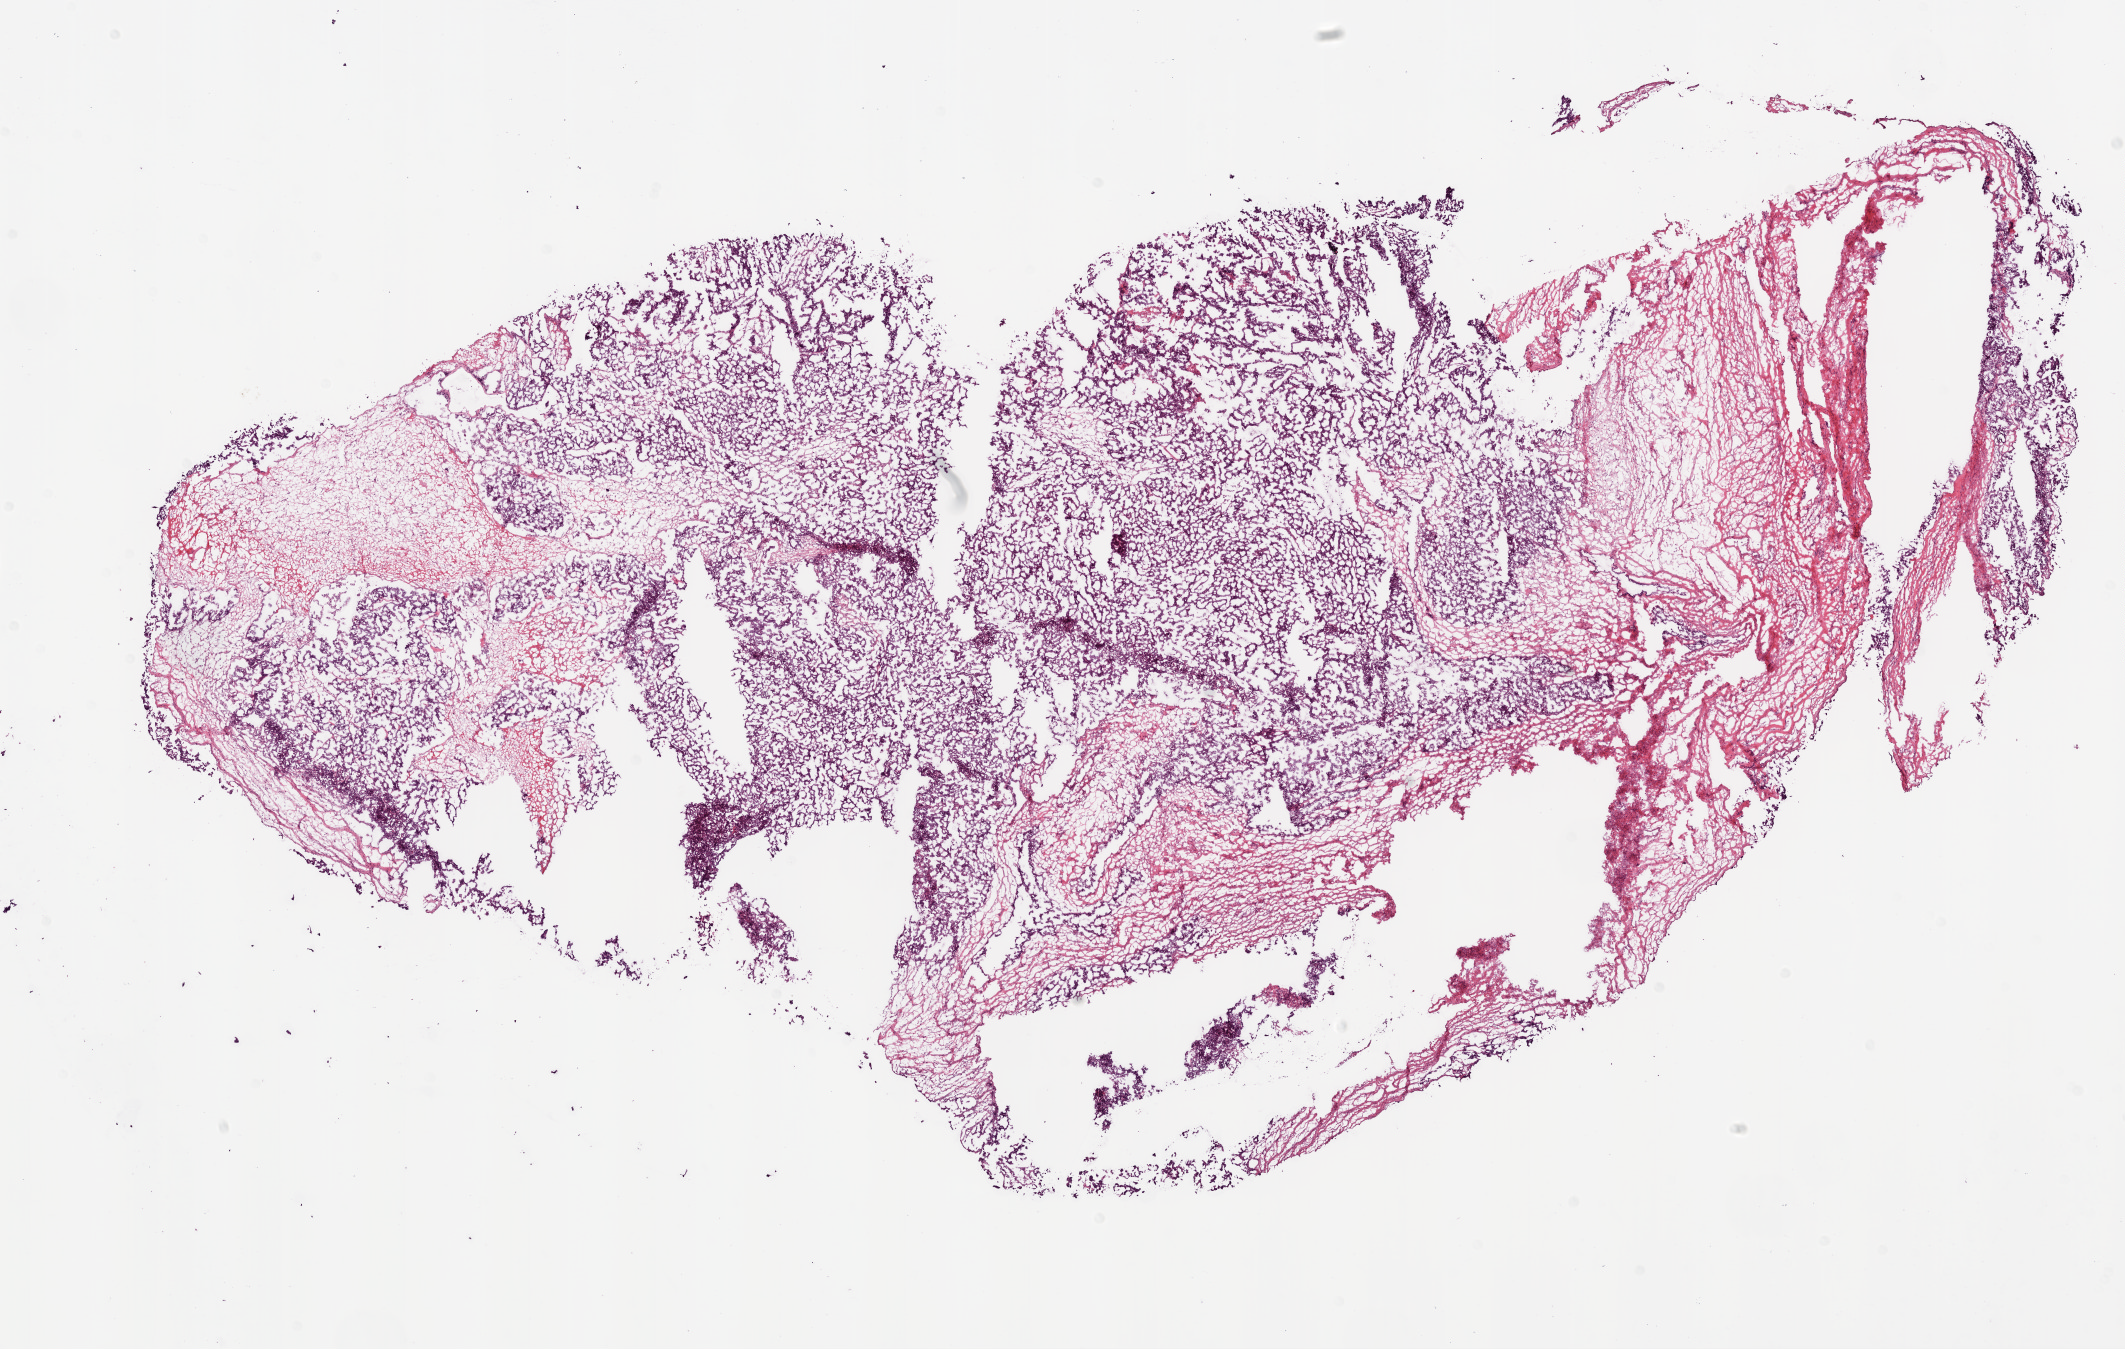
Digitized H&E tissue section (whole slide) — low-resolution overview of the scanned area, about 17.1 x 10.8 mm (from a 20x scan), frozen section from the bottom of the tissue portion, sample: primary tumour, ovary. Female patient; age at initial diagnosis 73 years.
Histologic diagnosis: Serous cystadenocarcinoma, NOS.